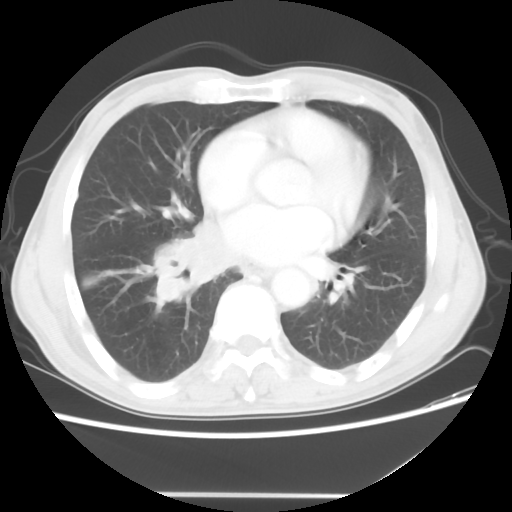
Chest CT, one axial slice; position 24 of 56 along the scan axis; lung window (W 1500 / L -600 HU); 5 mm slice thickness; 512 × 512 image matrix, field of view 344 × 344 mm. Male patient, age 65 years. From the clinical record (not read from this slice): clinical TNM (as recorded): T1c N3 M0; histopathological grade: G3.
Annotated regions visible in this slice (bounding box drawn by a radiologist):
- lung tumour (recorded histology: small cell carcinoma): box from (x=149, y=215) to (x=234, y=307) px